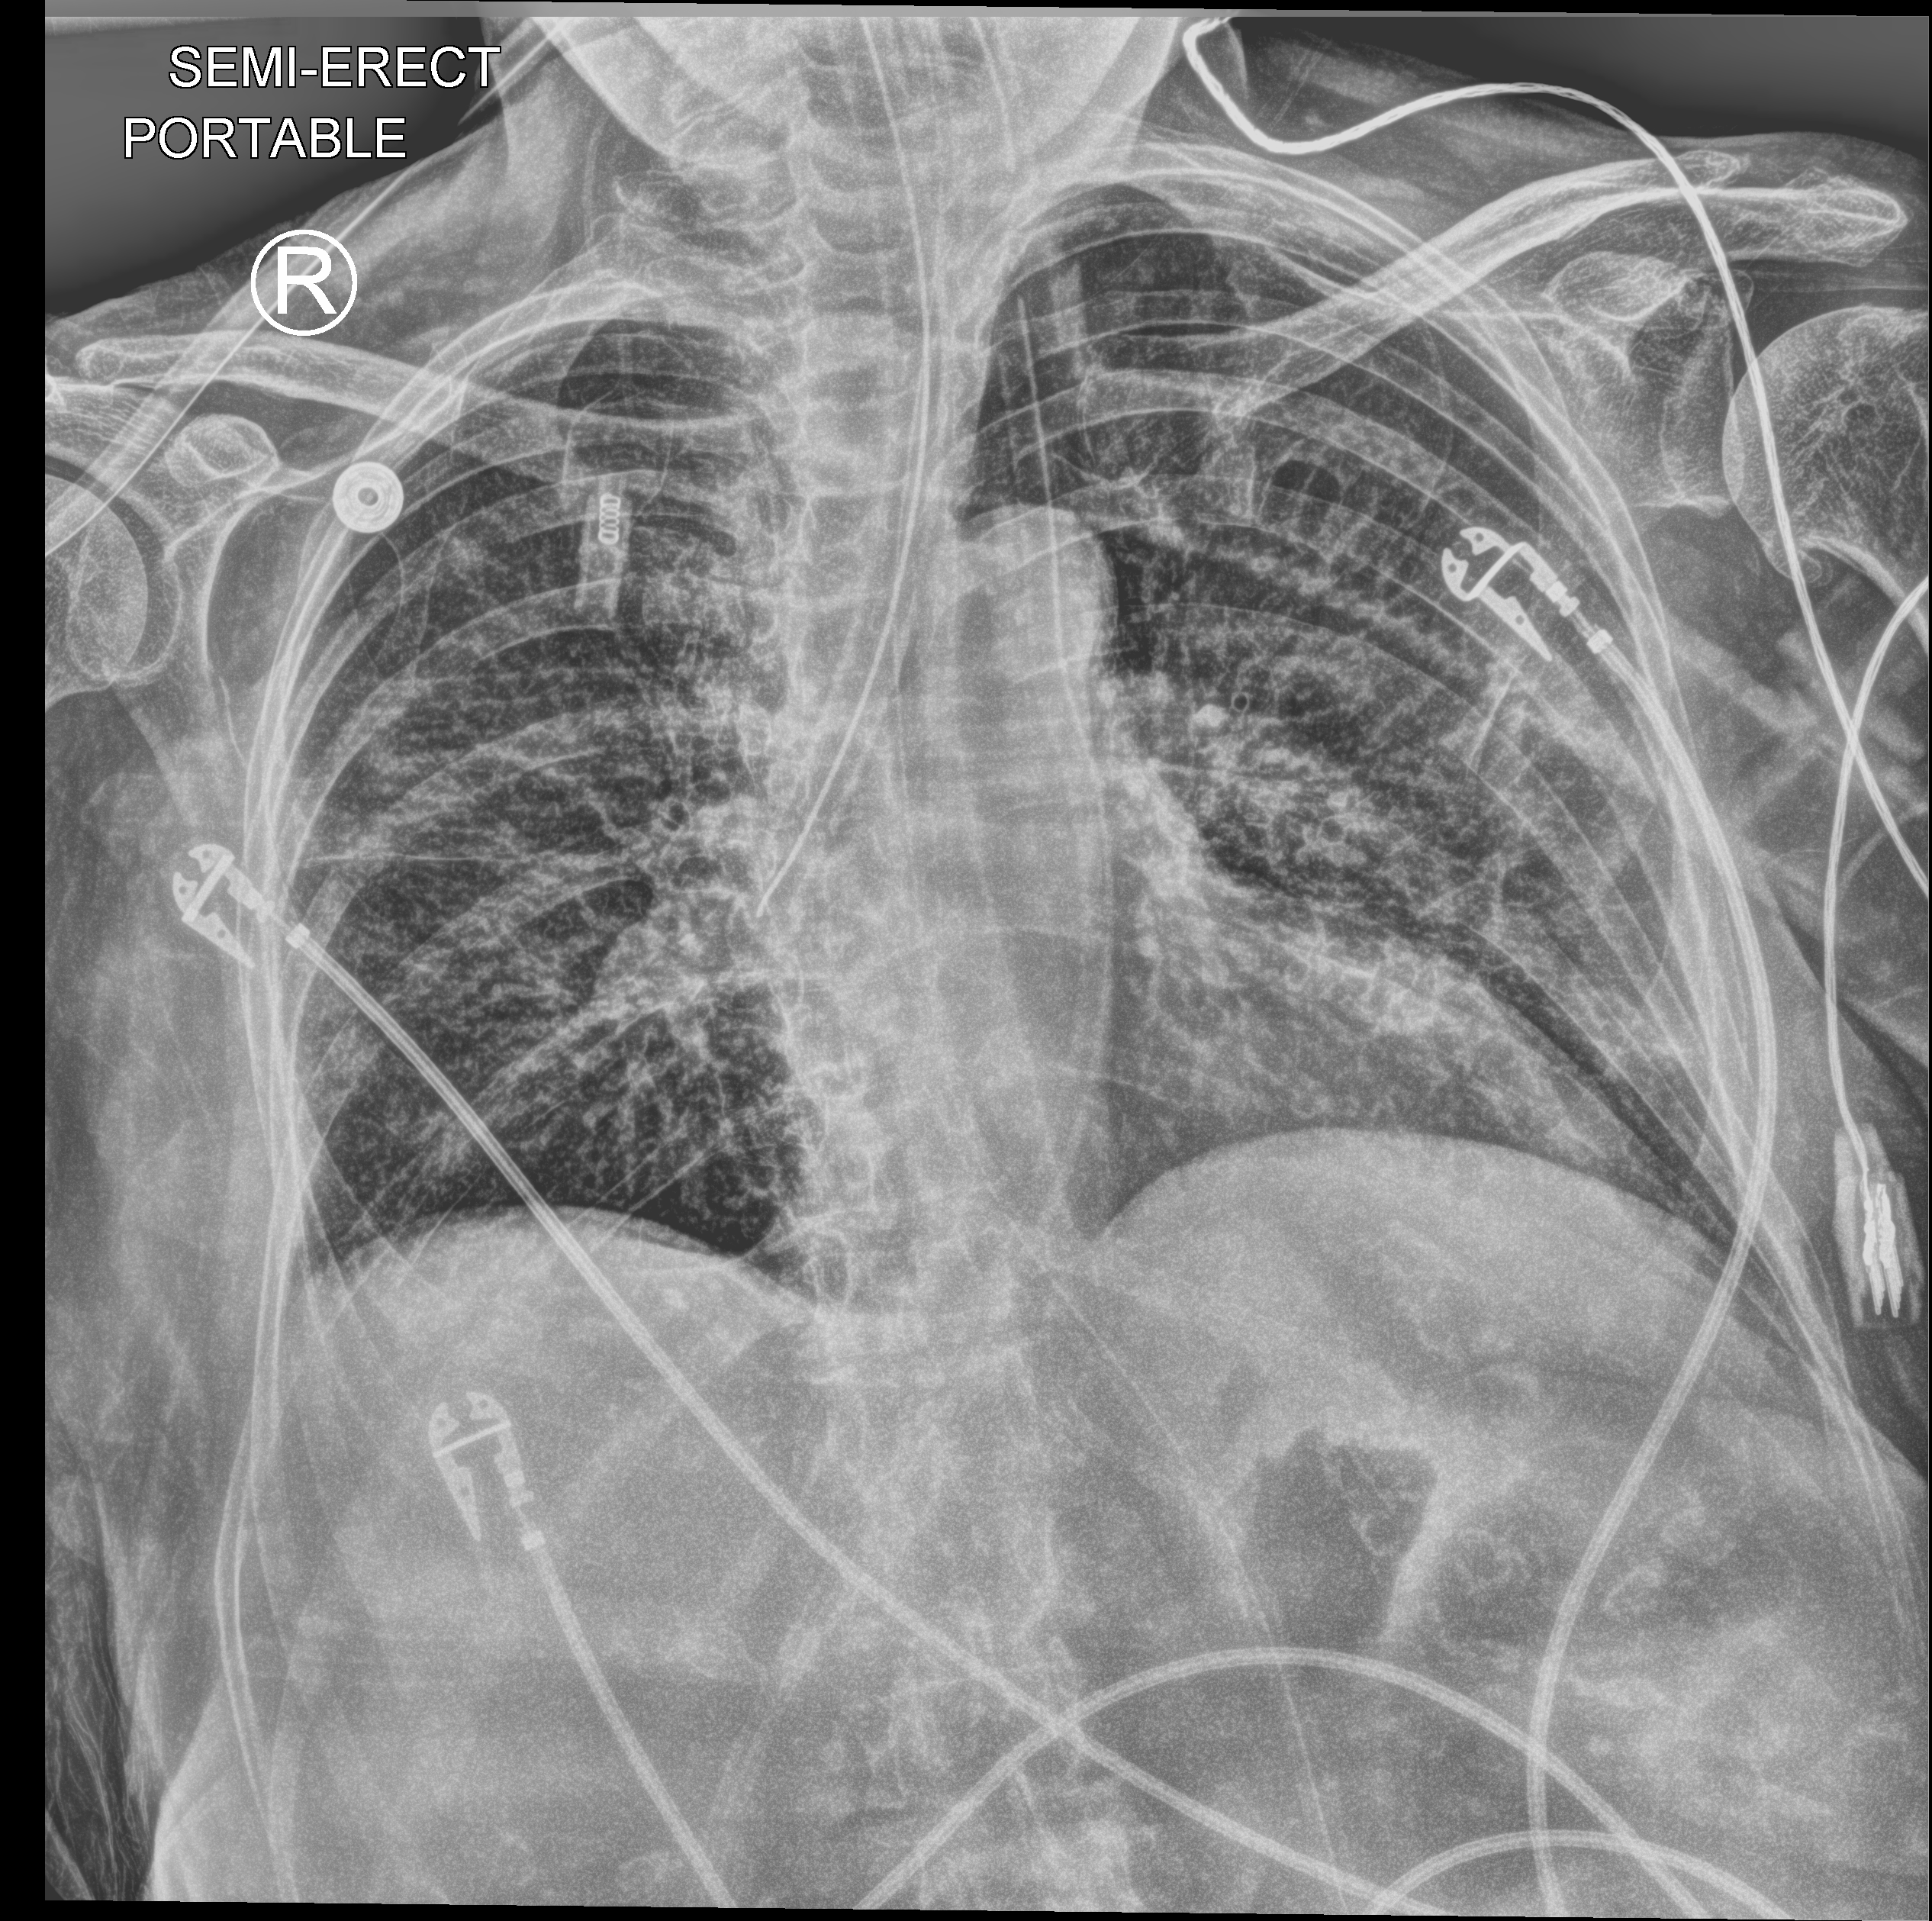
Chest X-ray (portable); anteroposterior (AP) projection. Patient hospitalised with COVID-19; female, aged 75–90 years.
From the hospital-stay record, not from the radiograph (when in the stay this image was taken is not recorded):
- admitted to intensive care during this hospital stay: yes